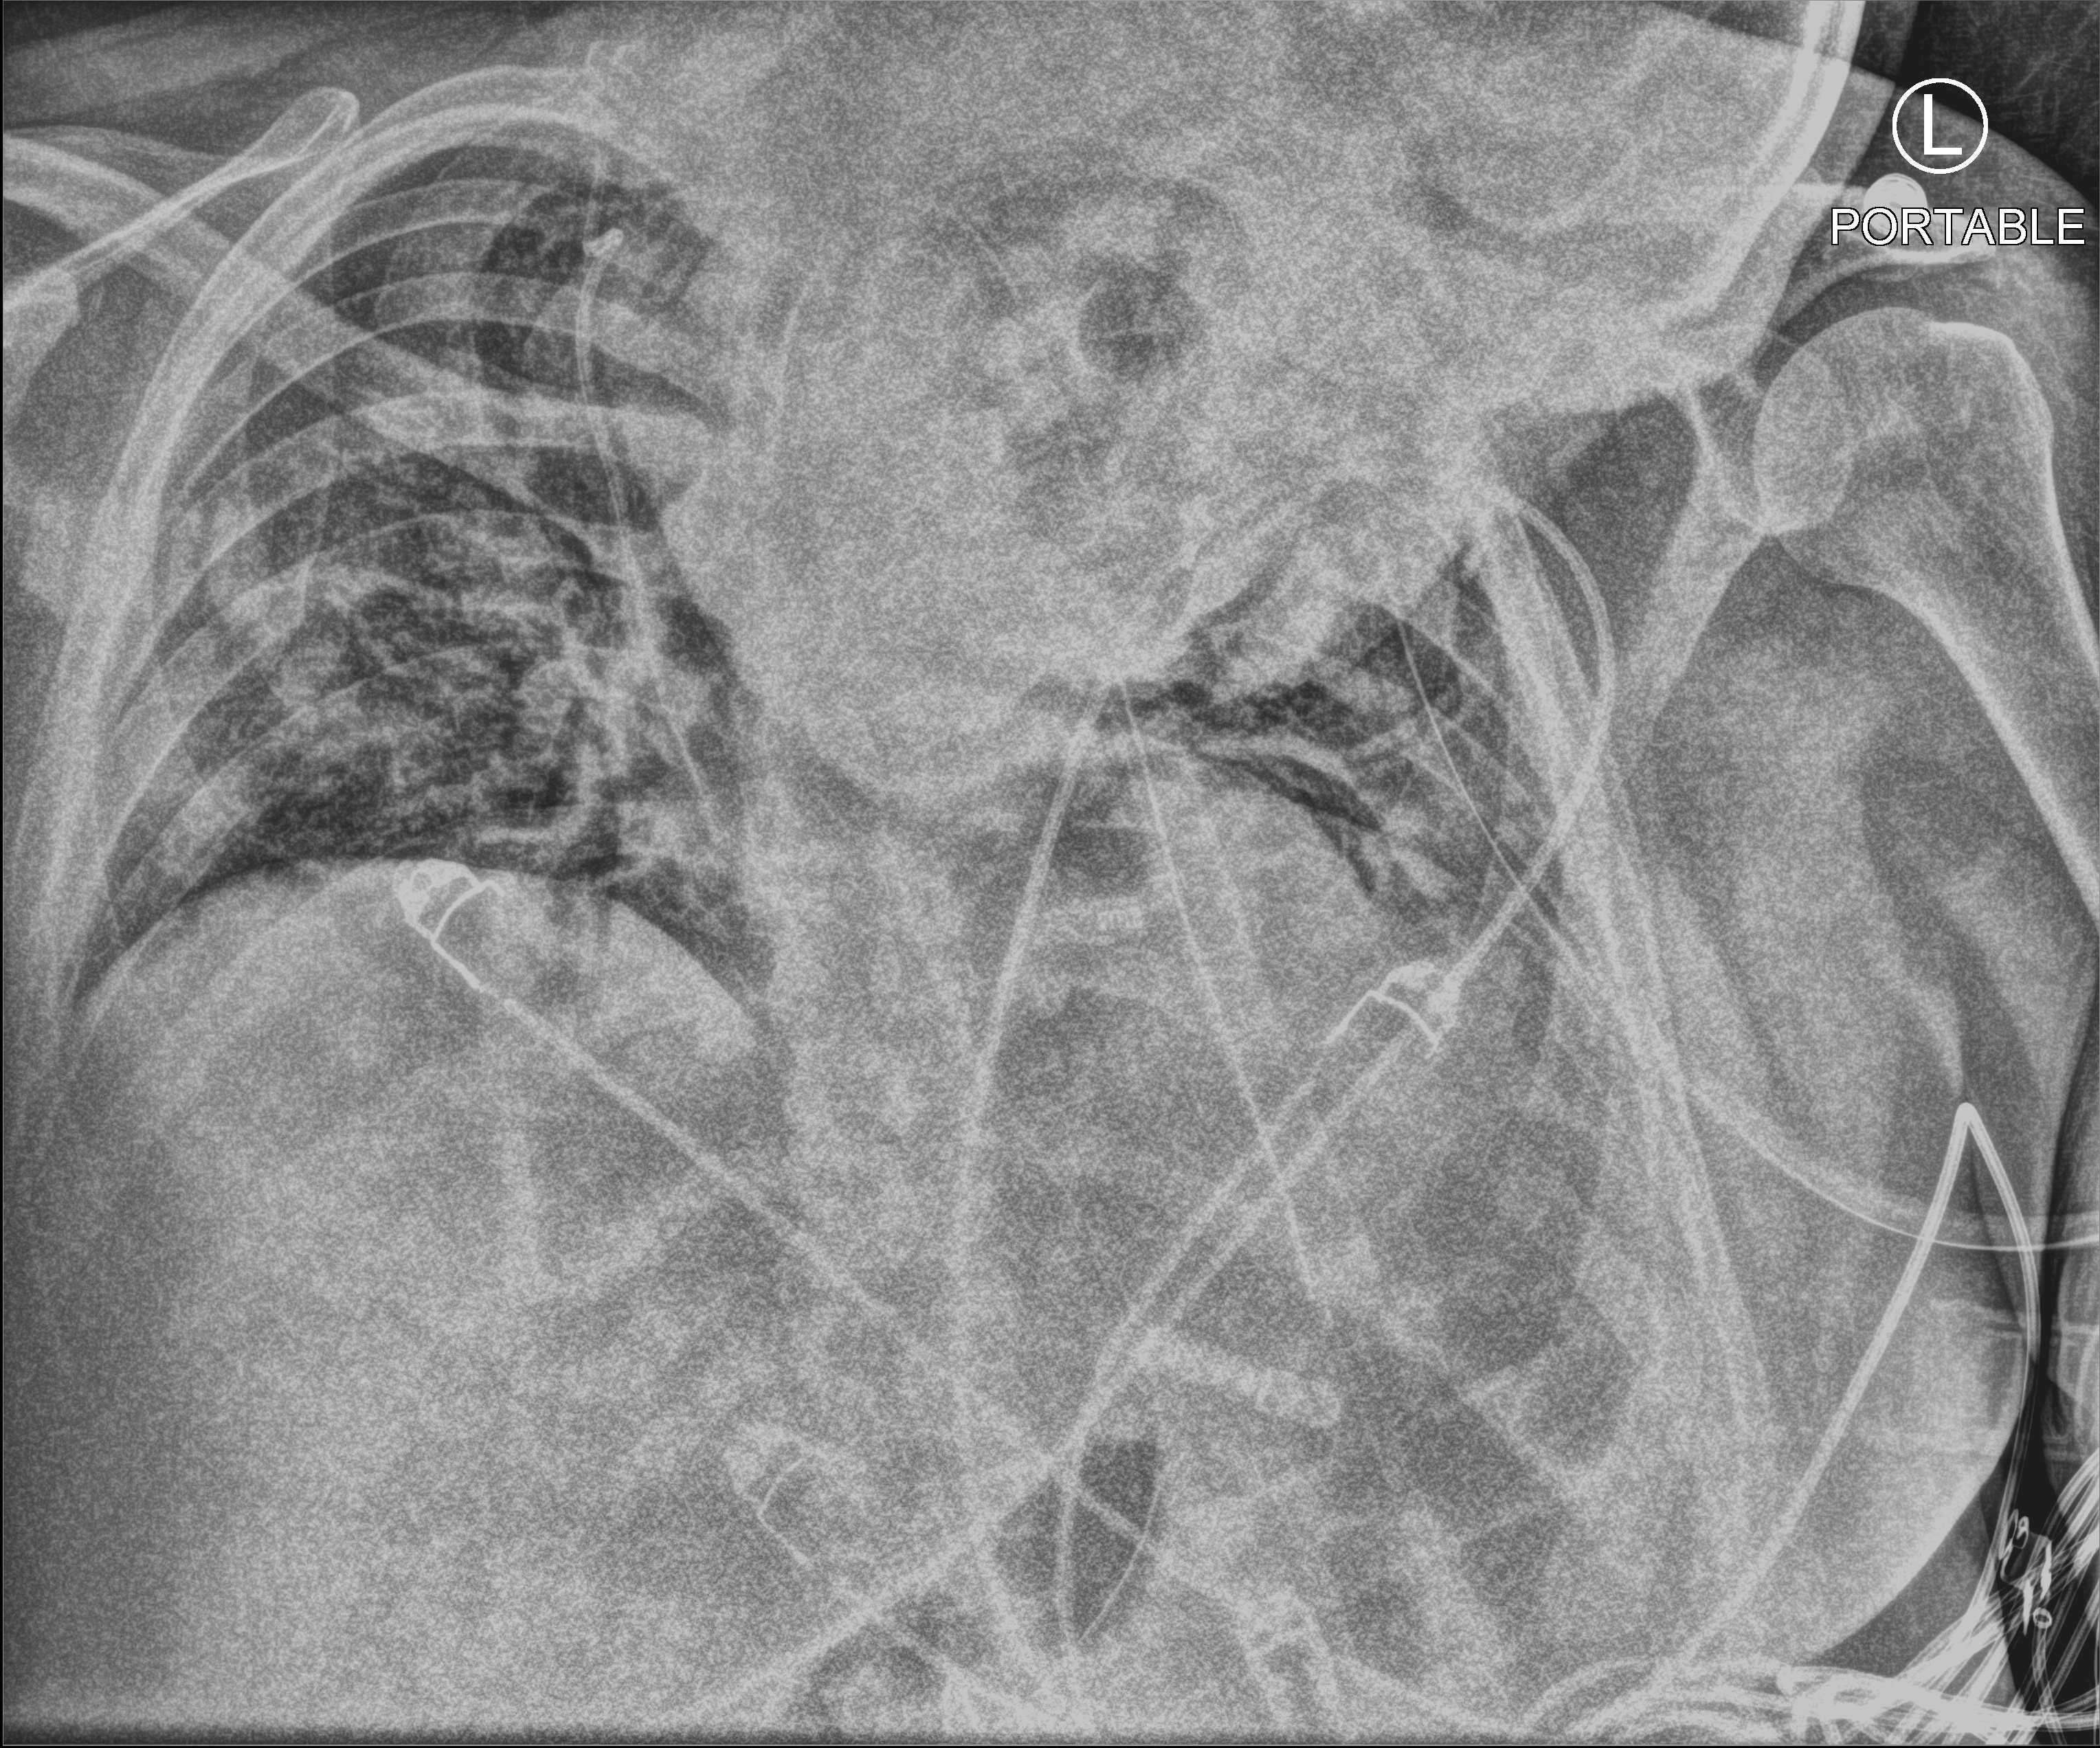
Chest X-ray (portable); anteroposterior (AP) projection. Male patient hospitalised with COVID-19, age 18–59 years.
Hospital-stay facts (about this admission, not read from this image; timing relative to this image not recorded):
- length of hospital stay: 39 days